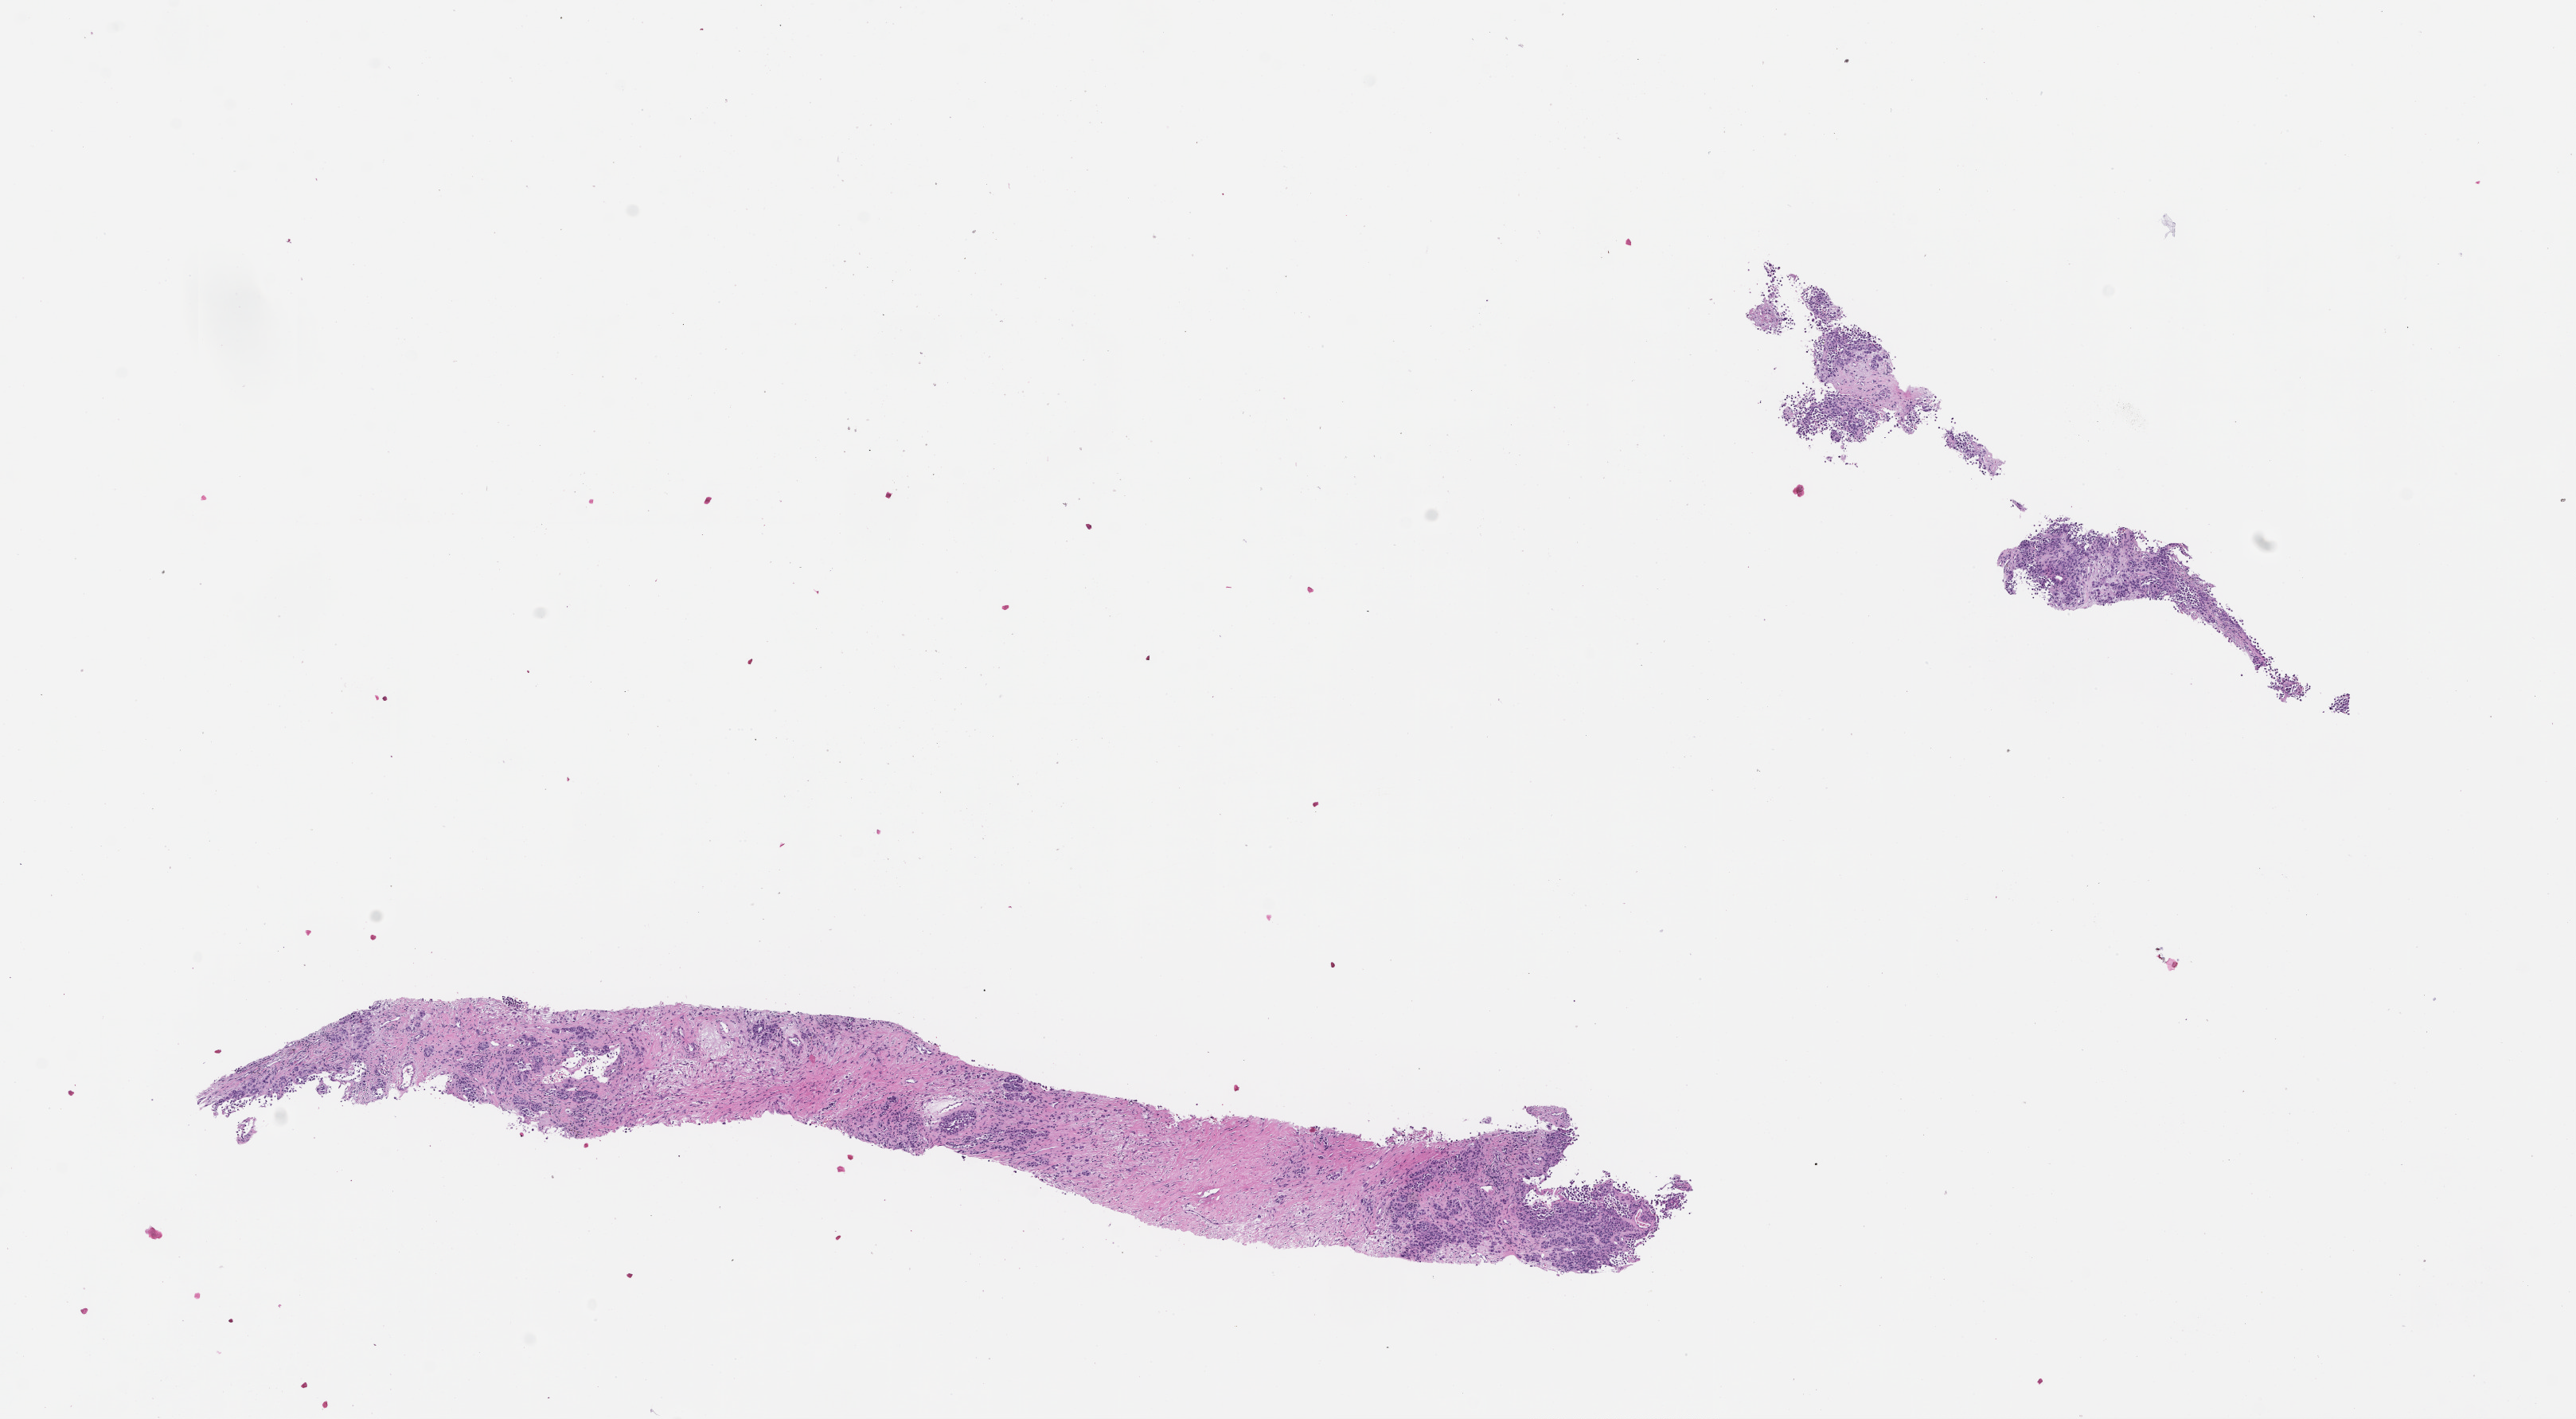
Digitized H&E-stained section, shown as a low-resolution overview of the whole scanned area (about 13.1 x 7.2 mm); formalin-fixed paraffin-embedded section; collected at baseline (before treatment). Male patient.
This section: metastatic tumor tissue. Primary diagnosis of the patient: Melanoma.